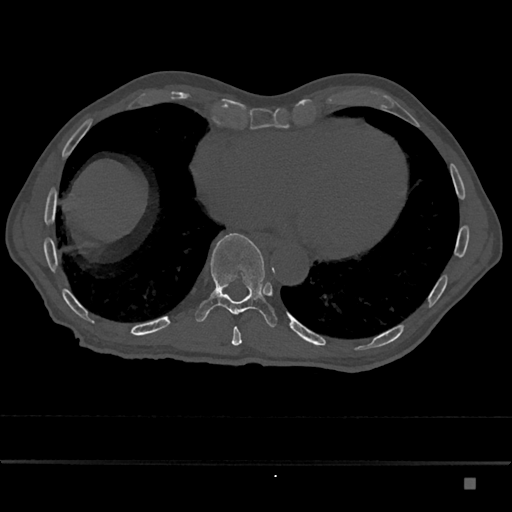
CT including the spine, one axial slice; slice 750 of 797 in the series (ordered by position); reconstruction kernel Br40s/3; bone window (W 1800 / L 400 HU); 0.5 mm slice thickness; 512 × 512 image matrix, field of view 390 × 390 mm. Male patient, age 72 years. Case-level facts recorded for this patient, not image findings: primary cancer: prostate.
Outlined on this slice (semi-automatically segmented with operator editing):
- T10 vertebra: bounding box (x1, y1, x2, y2) in pixels: (195, 233, 278, 328)
- T9 vertebra: (231, 326, 242, 346)